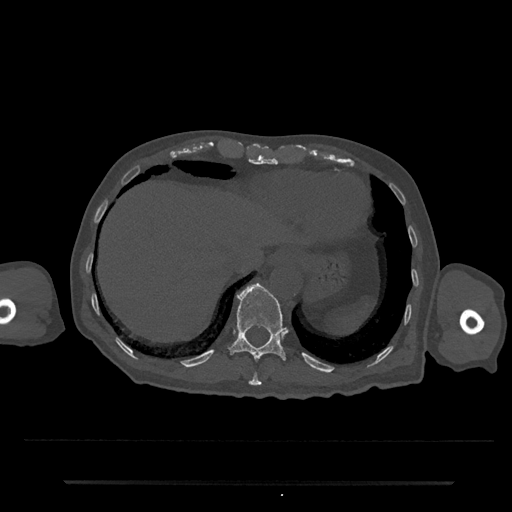
CT including the spine, one axial slice. Position 259 of 797 along the scan axis. 120 kVp. Bone window (W 1800 / L 400 HU). 0.5 mm slice thickness. 512 × 512 image matrix, field of view 427 × 427 mm. Male patient, age 74 years. Case-level facts recorded for this patient, not image findings: primary cancer: prostate.
Structures marked on this image (semi-automatically segmented with operator editing):
- T10 vertebra: box from (x=248, y=372) to (x=262, y=386) px
- T11 vertebra: (x=228, y=283)–(x=289, y=361)